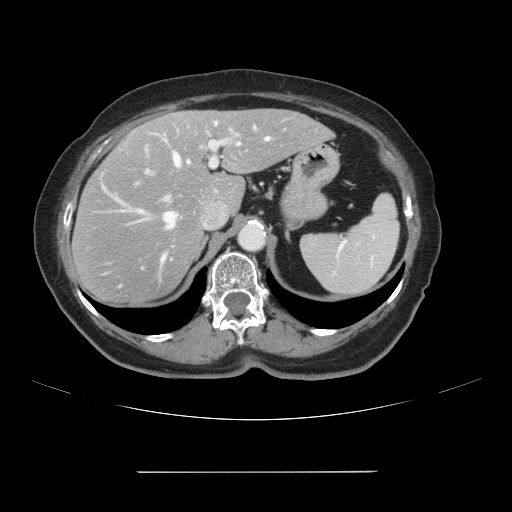
Contrast-enhanced abdominal CT, one axial slice; position 70 of 111 along the scan axis; intravenous contrast given; soft-tissue window (W 400 / L 40 HU); 2.5 mm slice thickness; 512 × 512 image matrix, field of view 400 × 400 mm. Female patient, age 74 years. Case-level facts recorded for this patient, not image findings: diagnosis: colorectal cancer liver metastases, imaged before liver resection; multiple liver metastases: yes.
Annotated regions visible in this slice (manually delineated by an expert):
- hepatic veins: box from (x=105, y=137) to (x=270, y=288) px
- liver: (x=74, y=110)–(x=331, y=305)
- planned liver remnant (the part of the liver to remain after resection): (x=152, y=110)–(x=331, y=211)
- portal vein (with intrahepatic branches): (x=146, y=122)–(x=237, y=201)